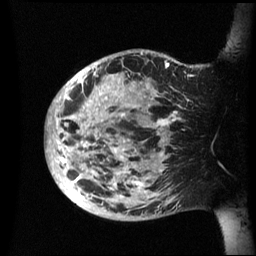
Breast MRI (dynamic contrast-enhanced), one sagittal slice. Slice 16 of 60 in the series (ordered by position). Dynamic contrast-enhanced series, image 2 of 3 at this slice position (ordered by acquisition). 1.5 T. TE 4.2 ms, TR 8.4 ms. 2.4 mm slice thickness. 256 × 256 image matrix, field of view 230 × 230 mm. Female patient, age 48 years.
Outlined on this slice (semi-automatic segmentation, software-assisted and operator-edited):
- analysis volume of interest (the breast-tissue region the enhancement analysis was run in; not a lesion): bounding box <46,49,202,221> (left, top, right, bottom; pixels)
- tumour enhancement mask (voxels above the 70 % enhancement threshold inside the analysis volume of interest): <46,52,198,207>